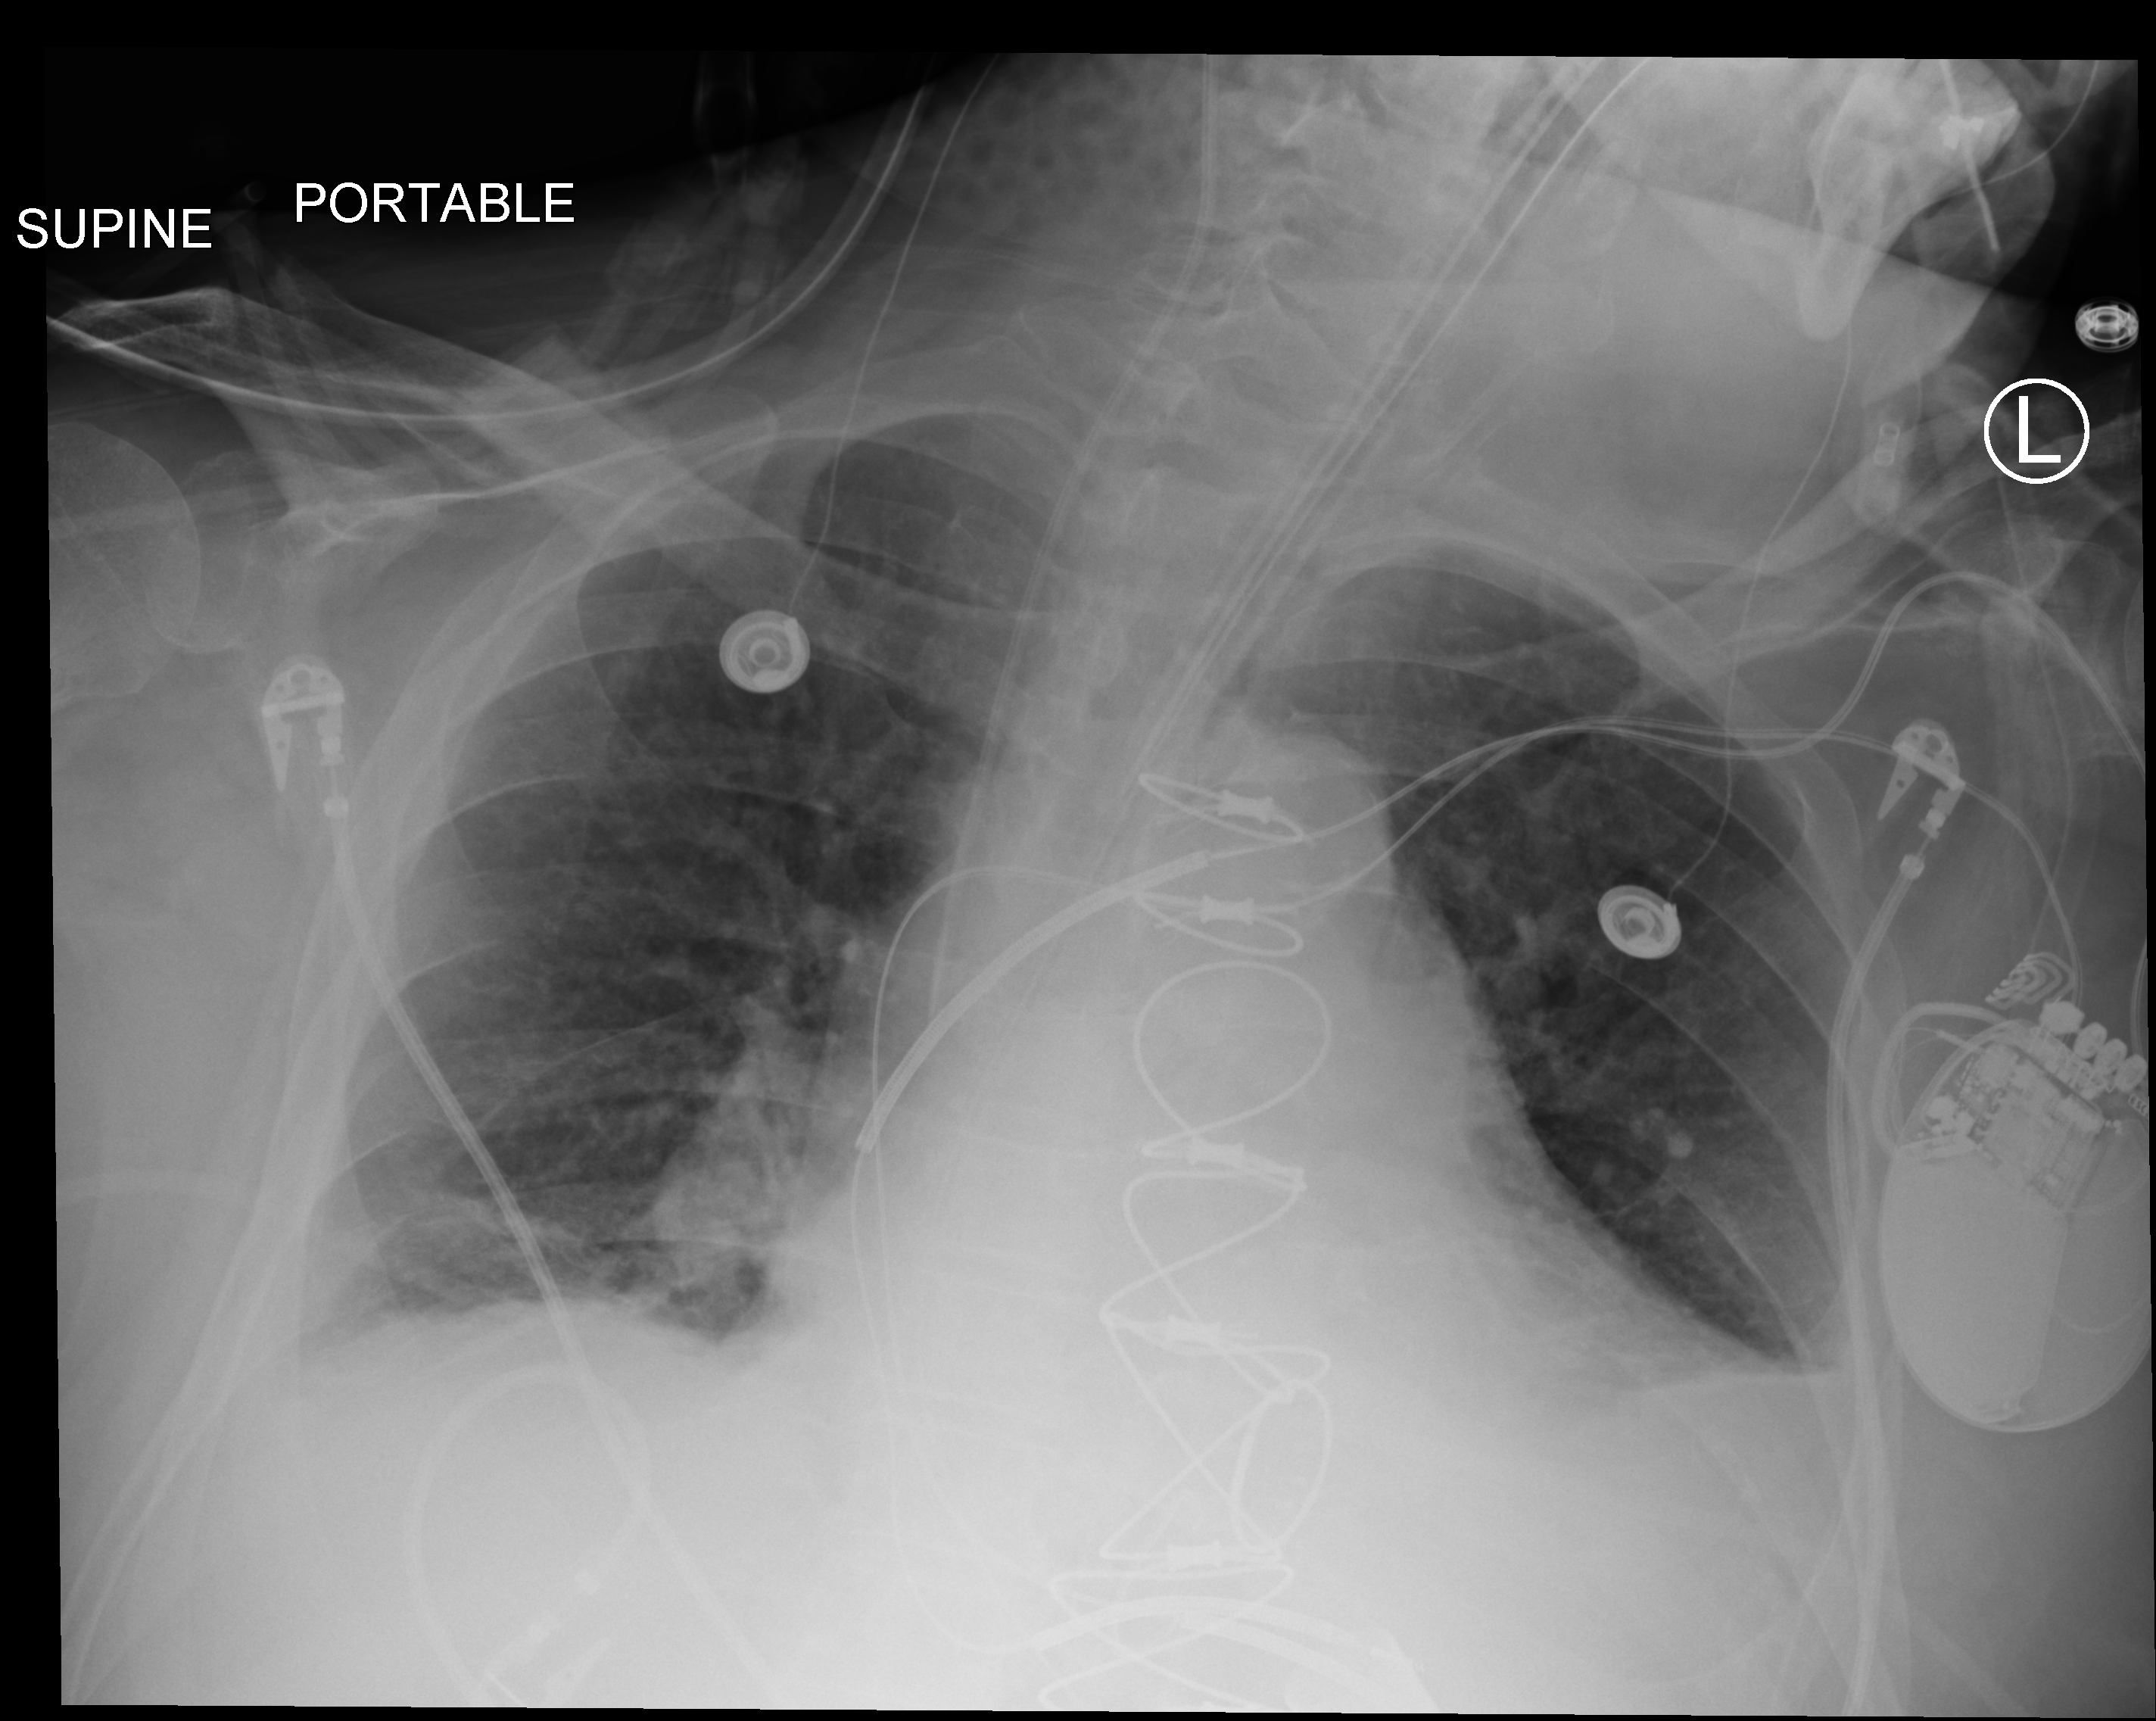
Chest X-ray (portable); anteroposterior (AP) projection. Male patient hospitalised with COVID-19, age 60–74 years.
Admission-level facts for this patient (not findings on this image; timing relative to this image not recorded): other chronic lung disease (admission record): no; length of hospital stay: 4 days; admitted to intensive care during this hospital stay: yes.